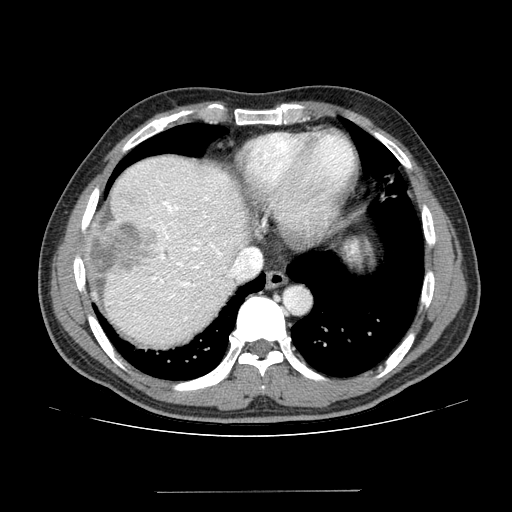
Contrast-enhanced abdominal CT (liver protocol), one axial slice; position 114 of 131 along the scan axis; one of 2 acquisitions stored at this slice position; soft-tissue window (W 400 / L 40 HU); 2.5 mm slice thickness; 512 × 512 image matrix, field of view 380 × 380 mm. From the clinical record (not read from this slice): diagnosis: hepatocellular carcinoma (patient treated with transarterial chemoembolisation; whether this scan precedes or follows treatment is not stated here); TNM stage (as recorded): Stage-I; Child-Pugh class: A; tumour differentiation: poorly differentiated; tumour nodularity: uninodular.
Structures marked on this image (semi-automatically segmented with operator editing):
- abdominal aorta: bounding box [x1, y1, x2, y2] px = [284, 286, 311, 314]
- liver parenchyma outside the tumour (the mass and vessels are separate outlines, so this box may not span the whole liver): [84, 154, 246, 346]
- mass: [90, 217, 156, 280]
- liver vessels: [109, 165, 226, 330]